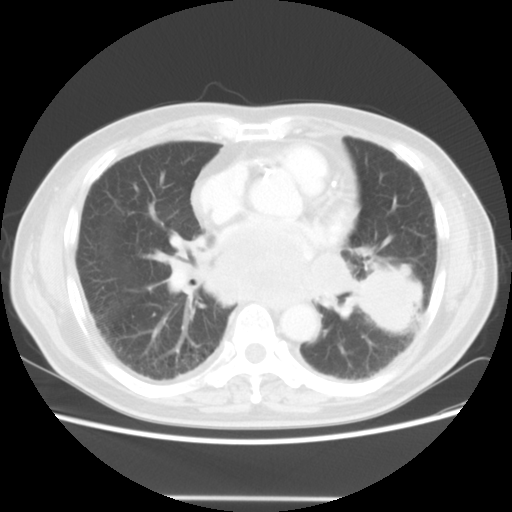
Chest CT, one axial slice. Position 23 of 56 along the scan axis. 140 kVp. Lung window (W 1500 / L -600 HU). 512 × 512 image matrix. Male patient, age 66 years. Case-level facts recorded for this patient, not image findings: clinical TNM (as recorded): T4 N3 M0; histopathological grade: G3.
Structures marked on this image (bounding box drawn by a radiologist):
- lung tumour (recorded histology: small cell carcinoma): bounding box (x1, y1, x2, y2) in pixels: (352, 258, 430, 336)